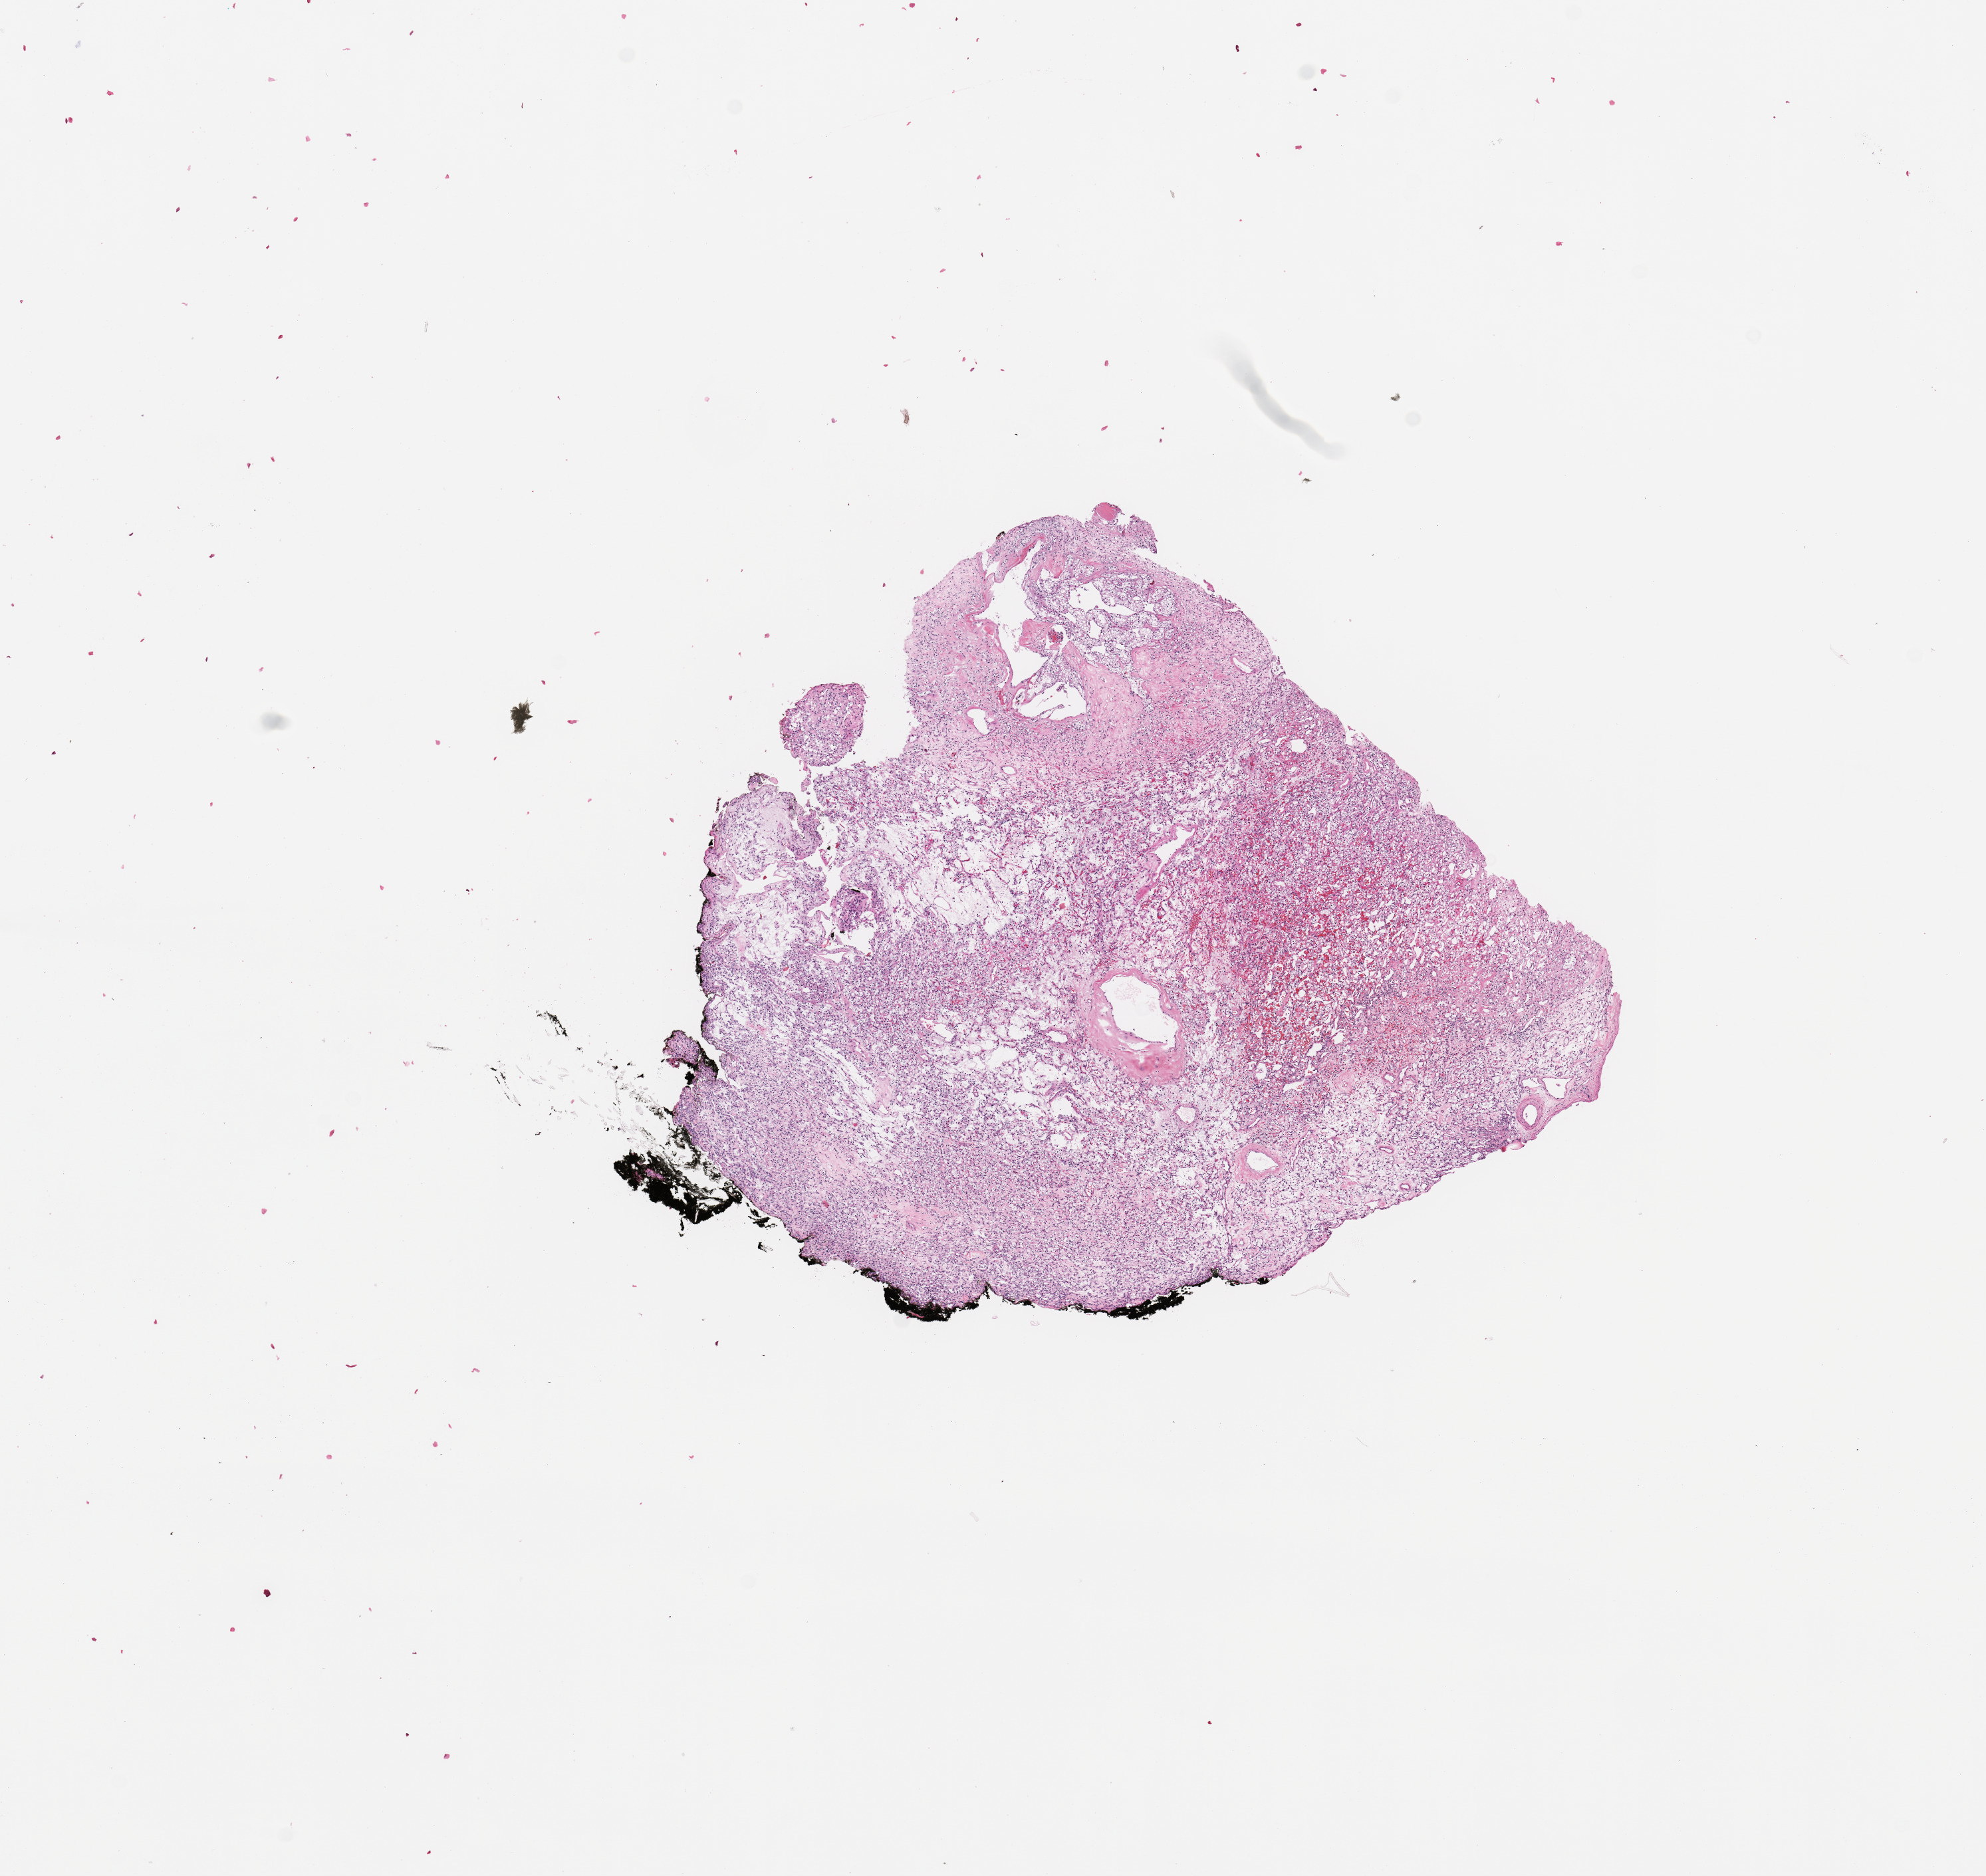
Digitized H&E-stained tissue section (whole slide) — shown as a low-resolution overview of the whole scanned area (about 11.8 x 11.2 mm), tumour tissue sample, sampled site: kidney. Male, 47 y/o. Histologic grade: G3 (poorly differentiated). Composition of this section per pathologist review: tumour nuclei 85%, necrosis 0%.
- AJCC pathologic stage: I
- histologic diagnosis: Renal cell carcinoma, NOS